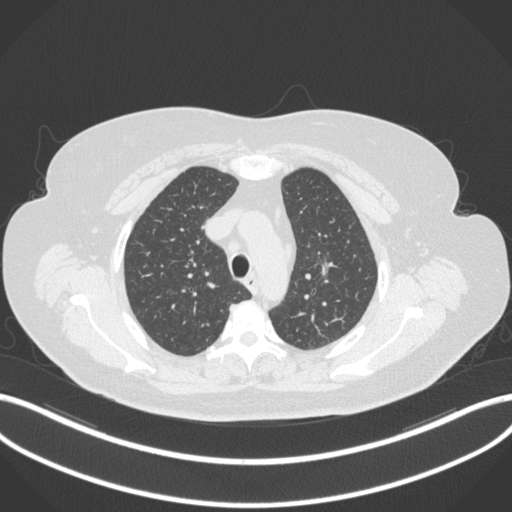
Chest CT, one axial slice; slice 257 of 310 in the series (ordered by position); reconstruction kernel B31f; lung window (W 1500 / L -600 HU); 512 × 512 image matrix. Patient: female, 70 years. Case-level facts recorded for this patient, not image findings: clinical TNM (as recorded): T1c N0 M0.
Structures marked on this image (bounding box drawn by a radiologist):
- lung tumour (recorded histology: adenocarcinoma): bounding box (x1, y1, x2, y2) in pixels: (316, 253, 339, 286)